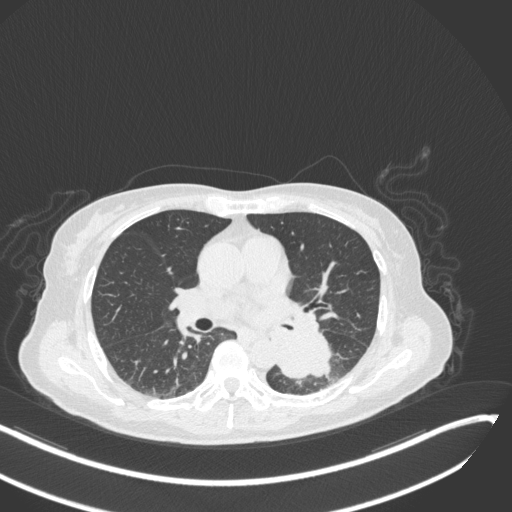
Chest CT, one axial slice; slice 149 of 342 in the series (ordered by position); 120 kVp; lung window (W 1500 / L -600 HU); 512 × 512 image matrix. Patient: female, 64 years. Case-level facts recorded for this patient, not image findings: clinical TNM (as recorded): T3 N1 M1; histopathological grade: G3.
Outlined on this slice (bounding box drawn by a radiologist):
- lung tumour (recorded histology: small cell carcinoma): bounding box (x1, y1, x2, y2) in pixels: (267, 326, 333, 383)